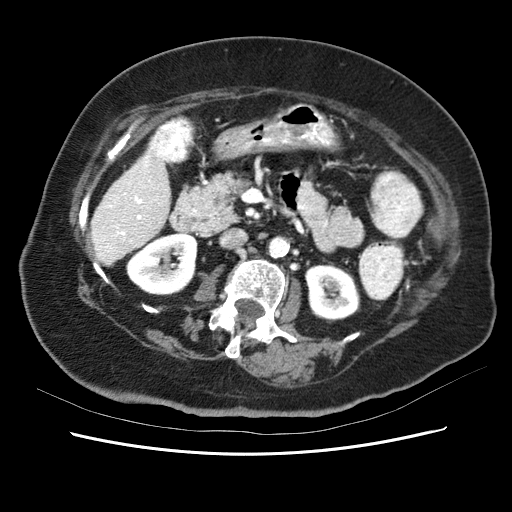
Contrast-enhanced abdominal CT (liver protocol), one axial slice. Position 17 of 62 along the scan axis. Reconstruction kernel STANDARD. Soft-tissue window (W 400 / L 40 HU). 2.5 mm slice thickness. 512 × 512 image matrix, field of view 340 × 340 mm. Case-level facts recorded for this patient, not image findings: diagnosis: hepatocellular carcinoma (patient treated with transarterial chemoembolisation; whether this scan precedes or follows treatment is not stated here); TNM stage (as recorded): Stage-I; Child-Pugh class: B; tumour nodularity: uninodular.
Annotated regions visible in this slice (semi-automatic segmentation, software-assisted and operator-edited):
- liver parenchyma outside the tumour (the mass and vessels are separate outlines, so this box may not span the whole liver): box from (x=90, y=143) to (x=172, y=270) px
- liver vessels: (x=94, y=152)–(x=166, y=258)